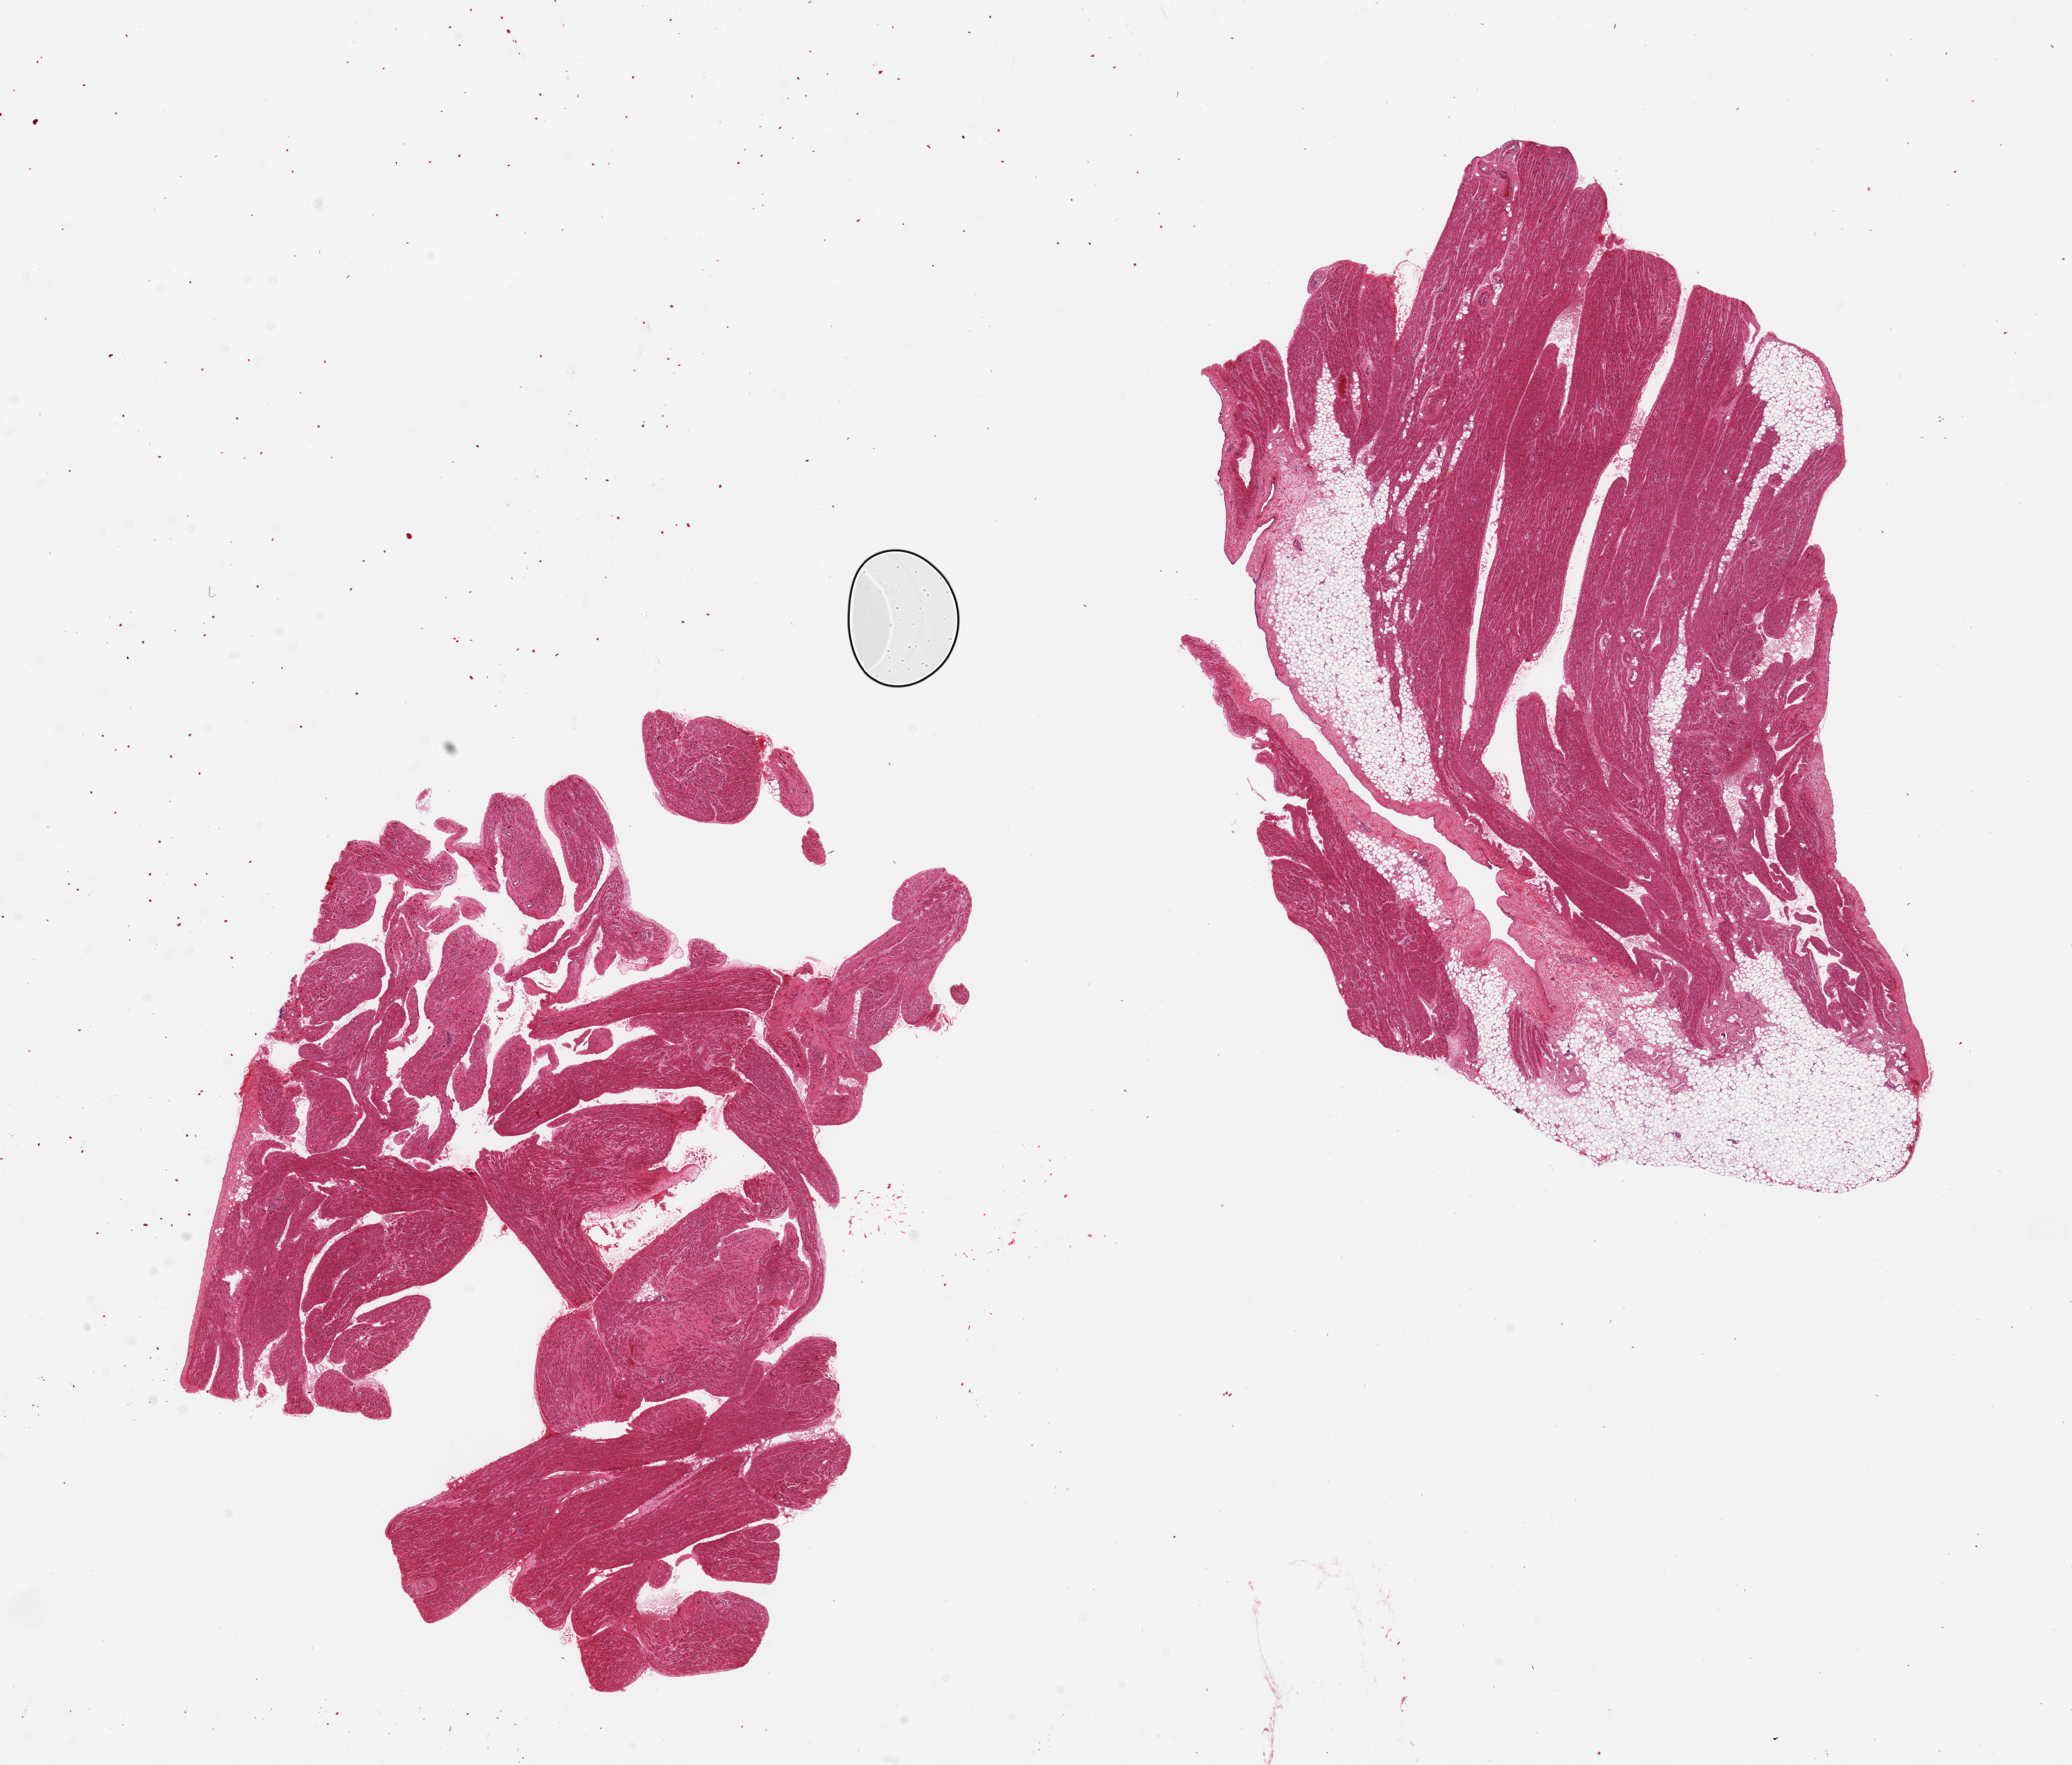
H&E whole-slide image, brightfield — shown as a low-resolution overview of the whole scanned area (about 23.6 x 20.1 mm, acquisition: 20x scan), PAXgene-fixed paraffin-embedded (PFPE) section, section of auricular appendage (target tissue), tissue donor sample.
Reviewer comment on this tissue sample: 2 pieces ~12x7mm.